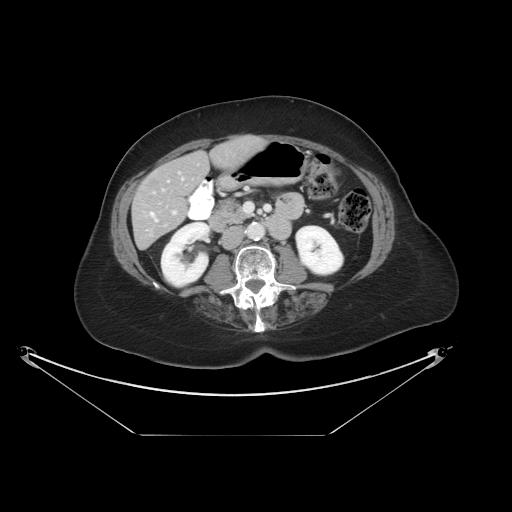
Contrast-enhanced abdominal CT, one axial slice; position 11 of 36 along the scan axis; reconstruction kernel STANDARD; 120 kVp; intravenous contrast given; soft-tissue window (W 400 / L 40 HU); 5 mm slice thickness; 512 × 512 image matrix. Female patient, age 70 years. Case-level facts recorded for this patient, not image findings: diagnosis: colorectal cancer liver metastases, imaged before liver resection; multiple liver metastases: no; largest metastasis: 2.5 cm; disease in both lobes: no.
Structures marked on this image (expert manual segmentation):
- hepatic veins: bounding box <151,178,184,222> (left, top, right, bottom; pixels)
- liver: <133,139,256,247>
- planned liver remnant (the part of the liver to remain after resection): <134,139,257,247>
- portal vein (with intrahepatic branches): <173,211,176,214>